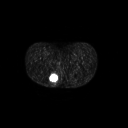
FDG PET of an extremity soft-tissue mass (from a PET/CT study), one axial slice. Position 20 of 267 along the scan axis. 3.27 mm slice thickness. 128 × 128 image matrix. Female patient, age 17 years. From the clinical record (not read from this slice): histological type: epithelioid sarcoma; grade: intermediate; site of the primary tumour: right buttock.
Outlined on this slice (expert contour drawn on MRI and transferred to this co-registered scan by the dataset authors):
- gross tumour volume including surrounding oedema: box from (x=49, y=73) to (x=60, y=87) px
- gross tumour volume (mass): (x=50, y=74)–(x=58, y=82)